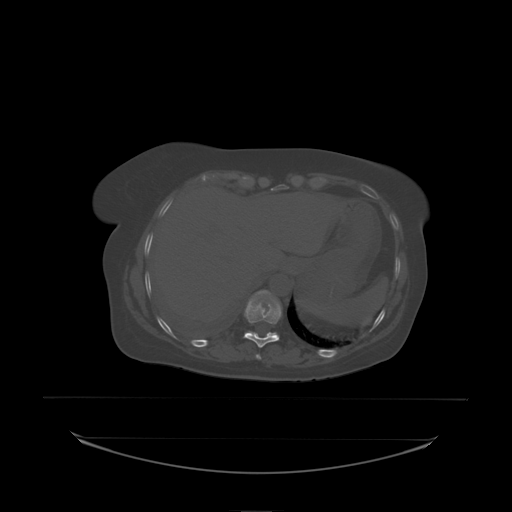
CT including the spine, one axial slice. Position 112 of 242 along the scan axis. Bone window (W 1800 / L 400 HU). 2.5 mm slice thickness. 512 × 512 image matrix. Patient: female, 53 years. From the clinical record (not read from this slice): primary cancer: lung.
Annotated regions visible in this slice (semi-automatic segmentation, software-assisted and operator-edited):
- T10 vertebra: bounding box <245,302,282,338> (left, top, right, bottom; pixels)
- T11 vertebra: <248,290,277,335>